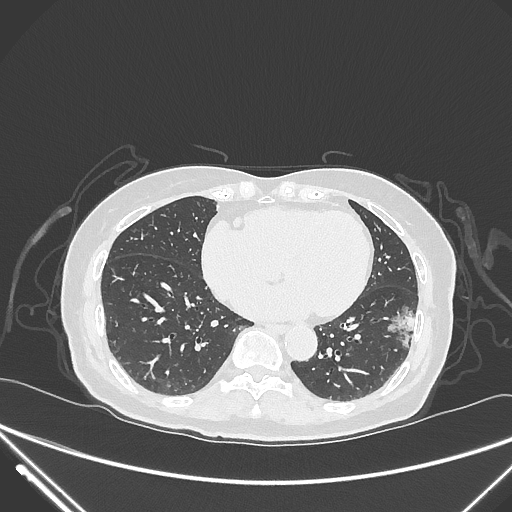
Chest CT, one axial slice; slice 113 of 310 in the series (ordered by position); lung window (W 1500 / L -600 HU); 512 × 512 image matrix. Female patient, age 82 years. Case-level facts recorded for this patient, not image findings: clinical TNM (as recorded): T1c N0 M0; histopathological grade: G2.
Annotated regions visible in this slice (bounding box drawn by a radiologist):
- lung tumour (recorded histology: adenocarcinoma): bounding box [x1, y1, x2, y2] px = [384, 297, 419, 351]